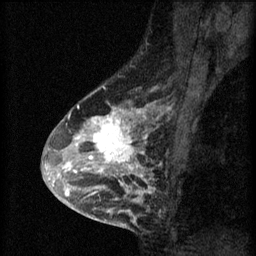
Breast MRI (dynamic contrast-enhanced), one sagittal slice; position 39 of 60 along the scan axis; 3 images stored at this slice position (order not interpretable as contrast timing); 1.5 T; TE 4.2 ms, TR 8.2 ms; 2 mm slice thickness; 256 × 256 image matrix, field of view 180 × 180 mm. Patient: female, 45 years.
Structures marked on this image (semi-automatic segmentation, software-assisted and operator-edited):
- analysis volume of interest (the breast-tissue region the enhancement analysis was run in; not a lesion): bounding box <54,104,159,217> (left, top, right, bottom; pixels)
- tumour enhancement mask (voxels above the 70 % enhancement threshold inside the analysis volume of interest): <54,104,153,213>